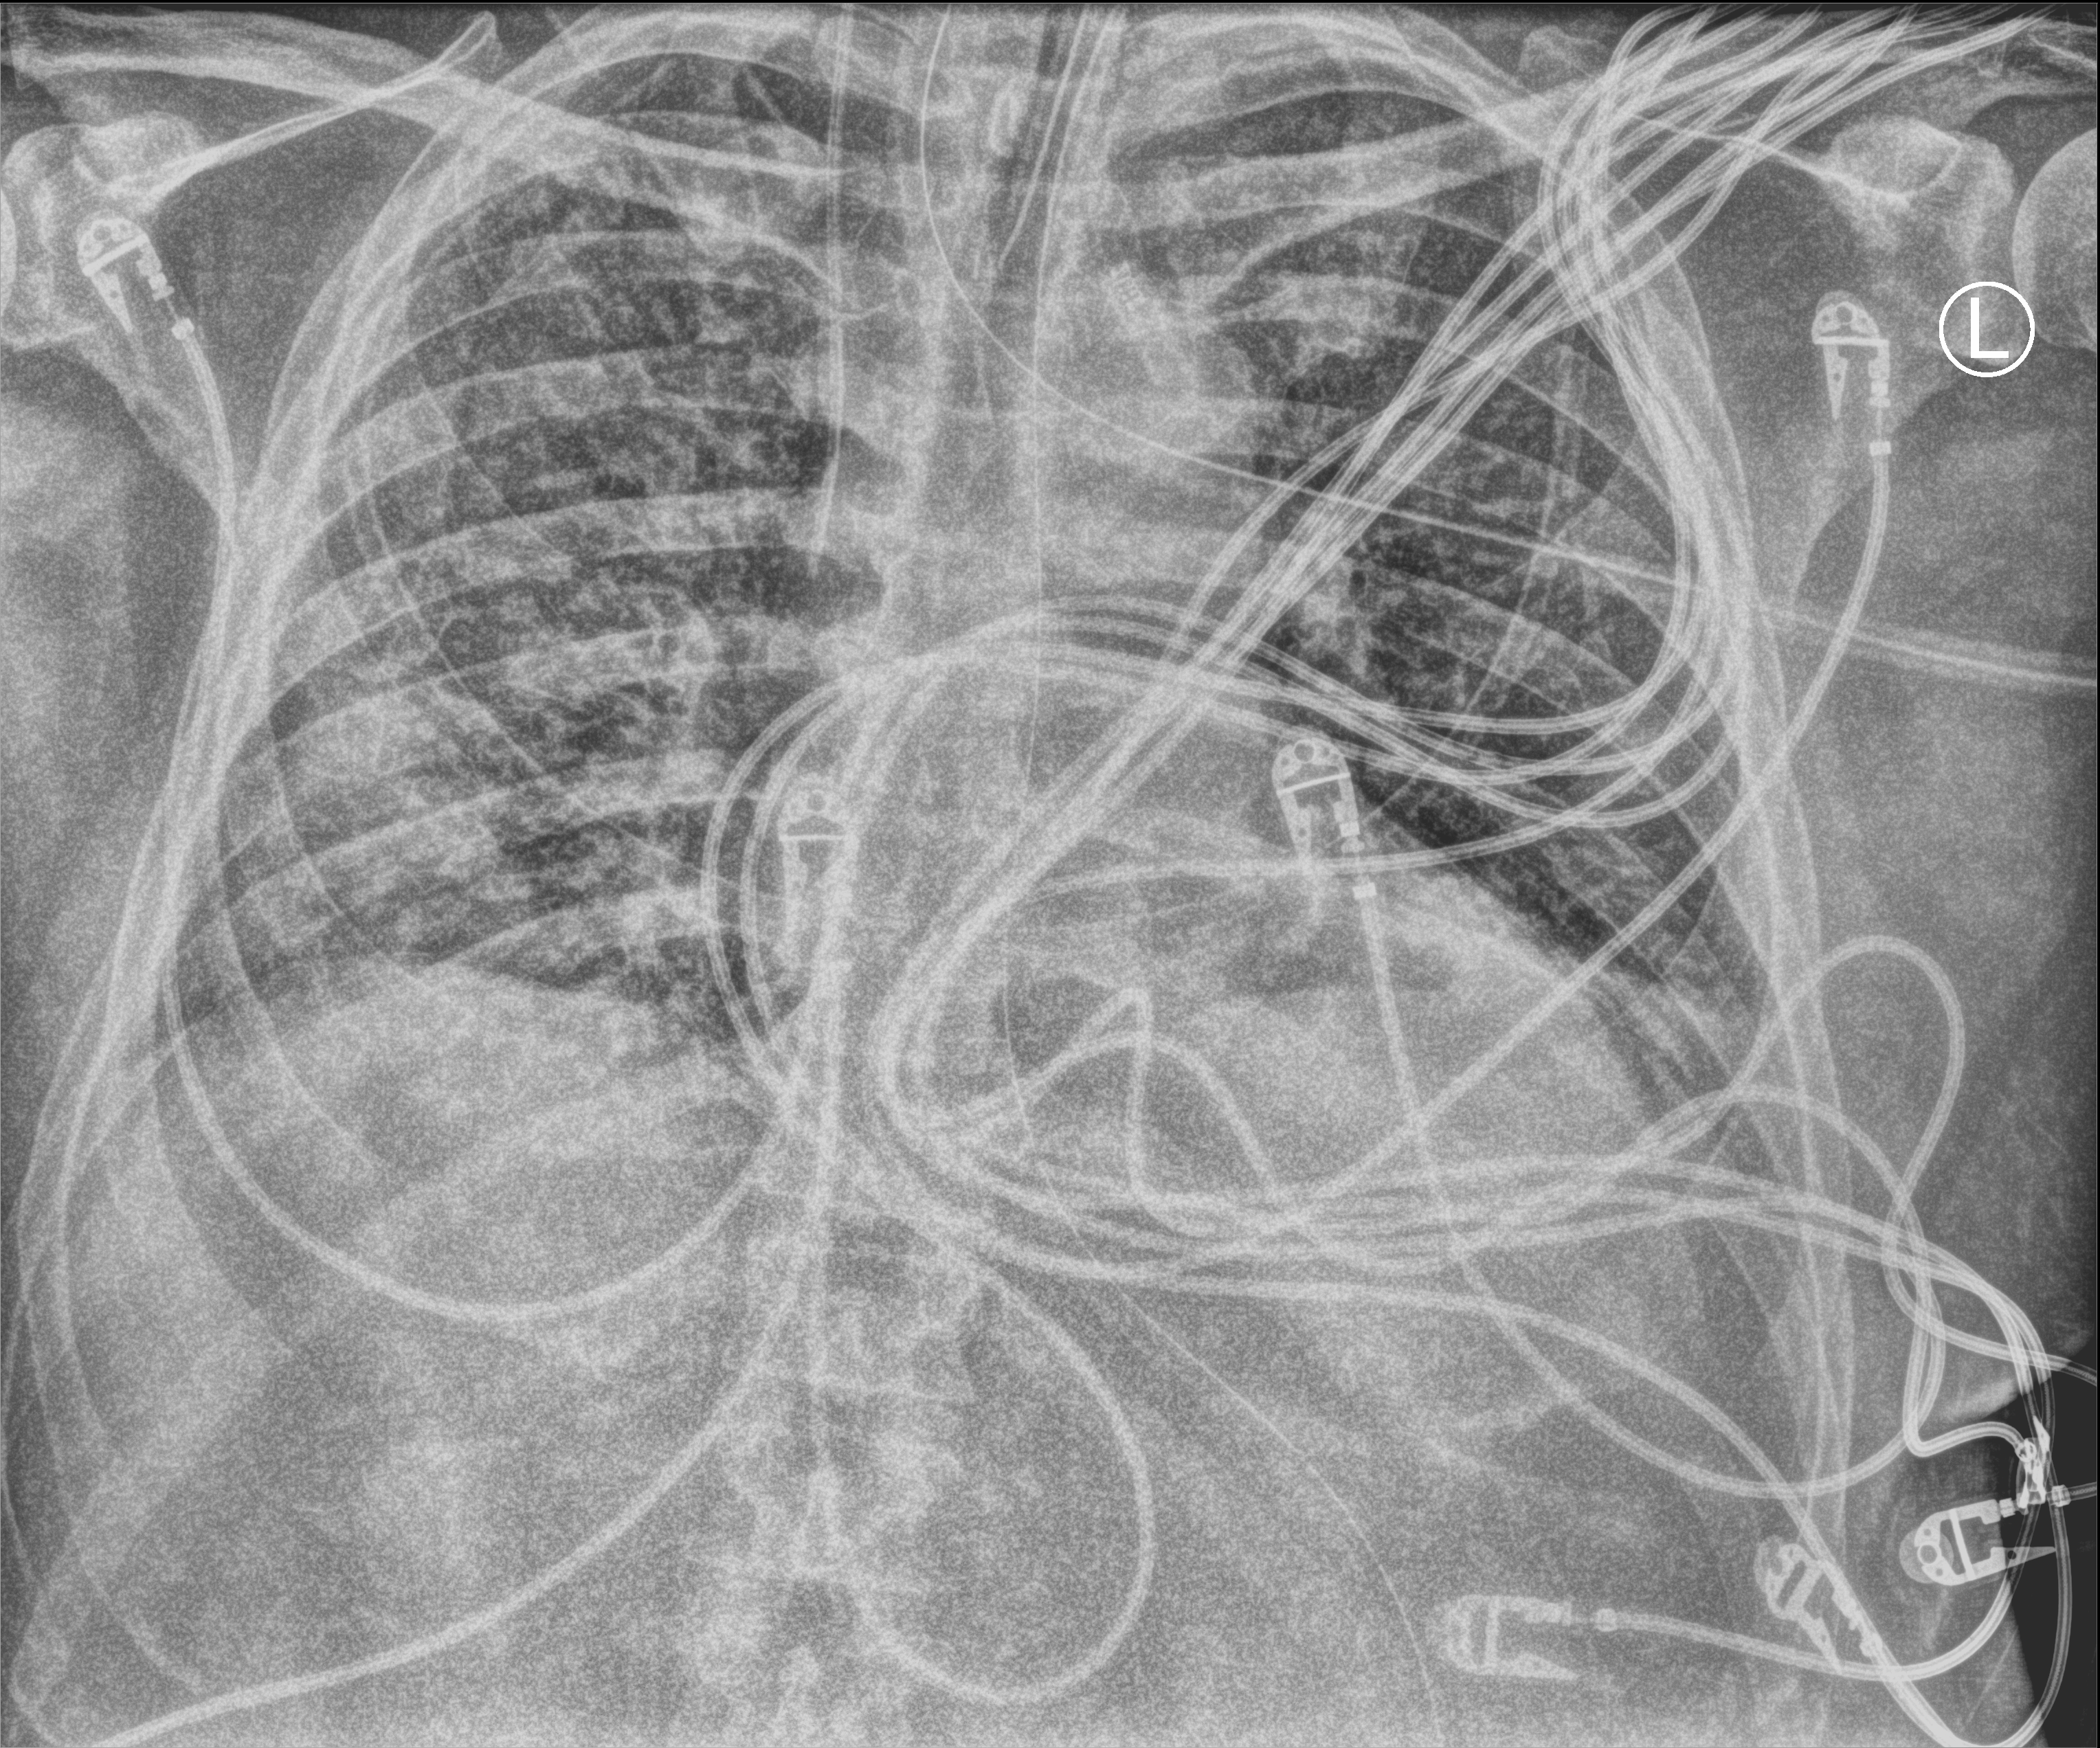
Portable chest radiograph, anteroposterior (AP) projection. Male patient hospitalised with COVID-19, age 60–74 years.
Hospital-stay facts (about this admission, not read from this image; timing relative to this image not recorded): mechanically ventilated during this hospital stay: yes.